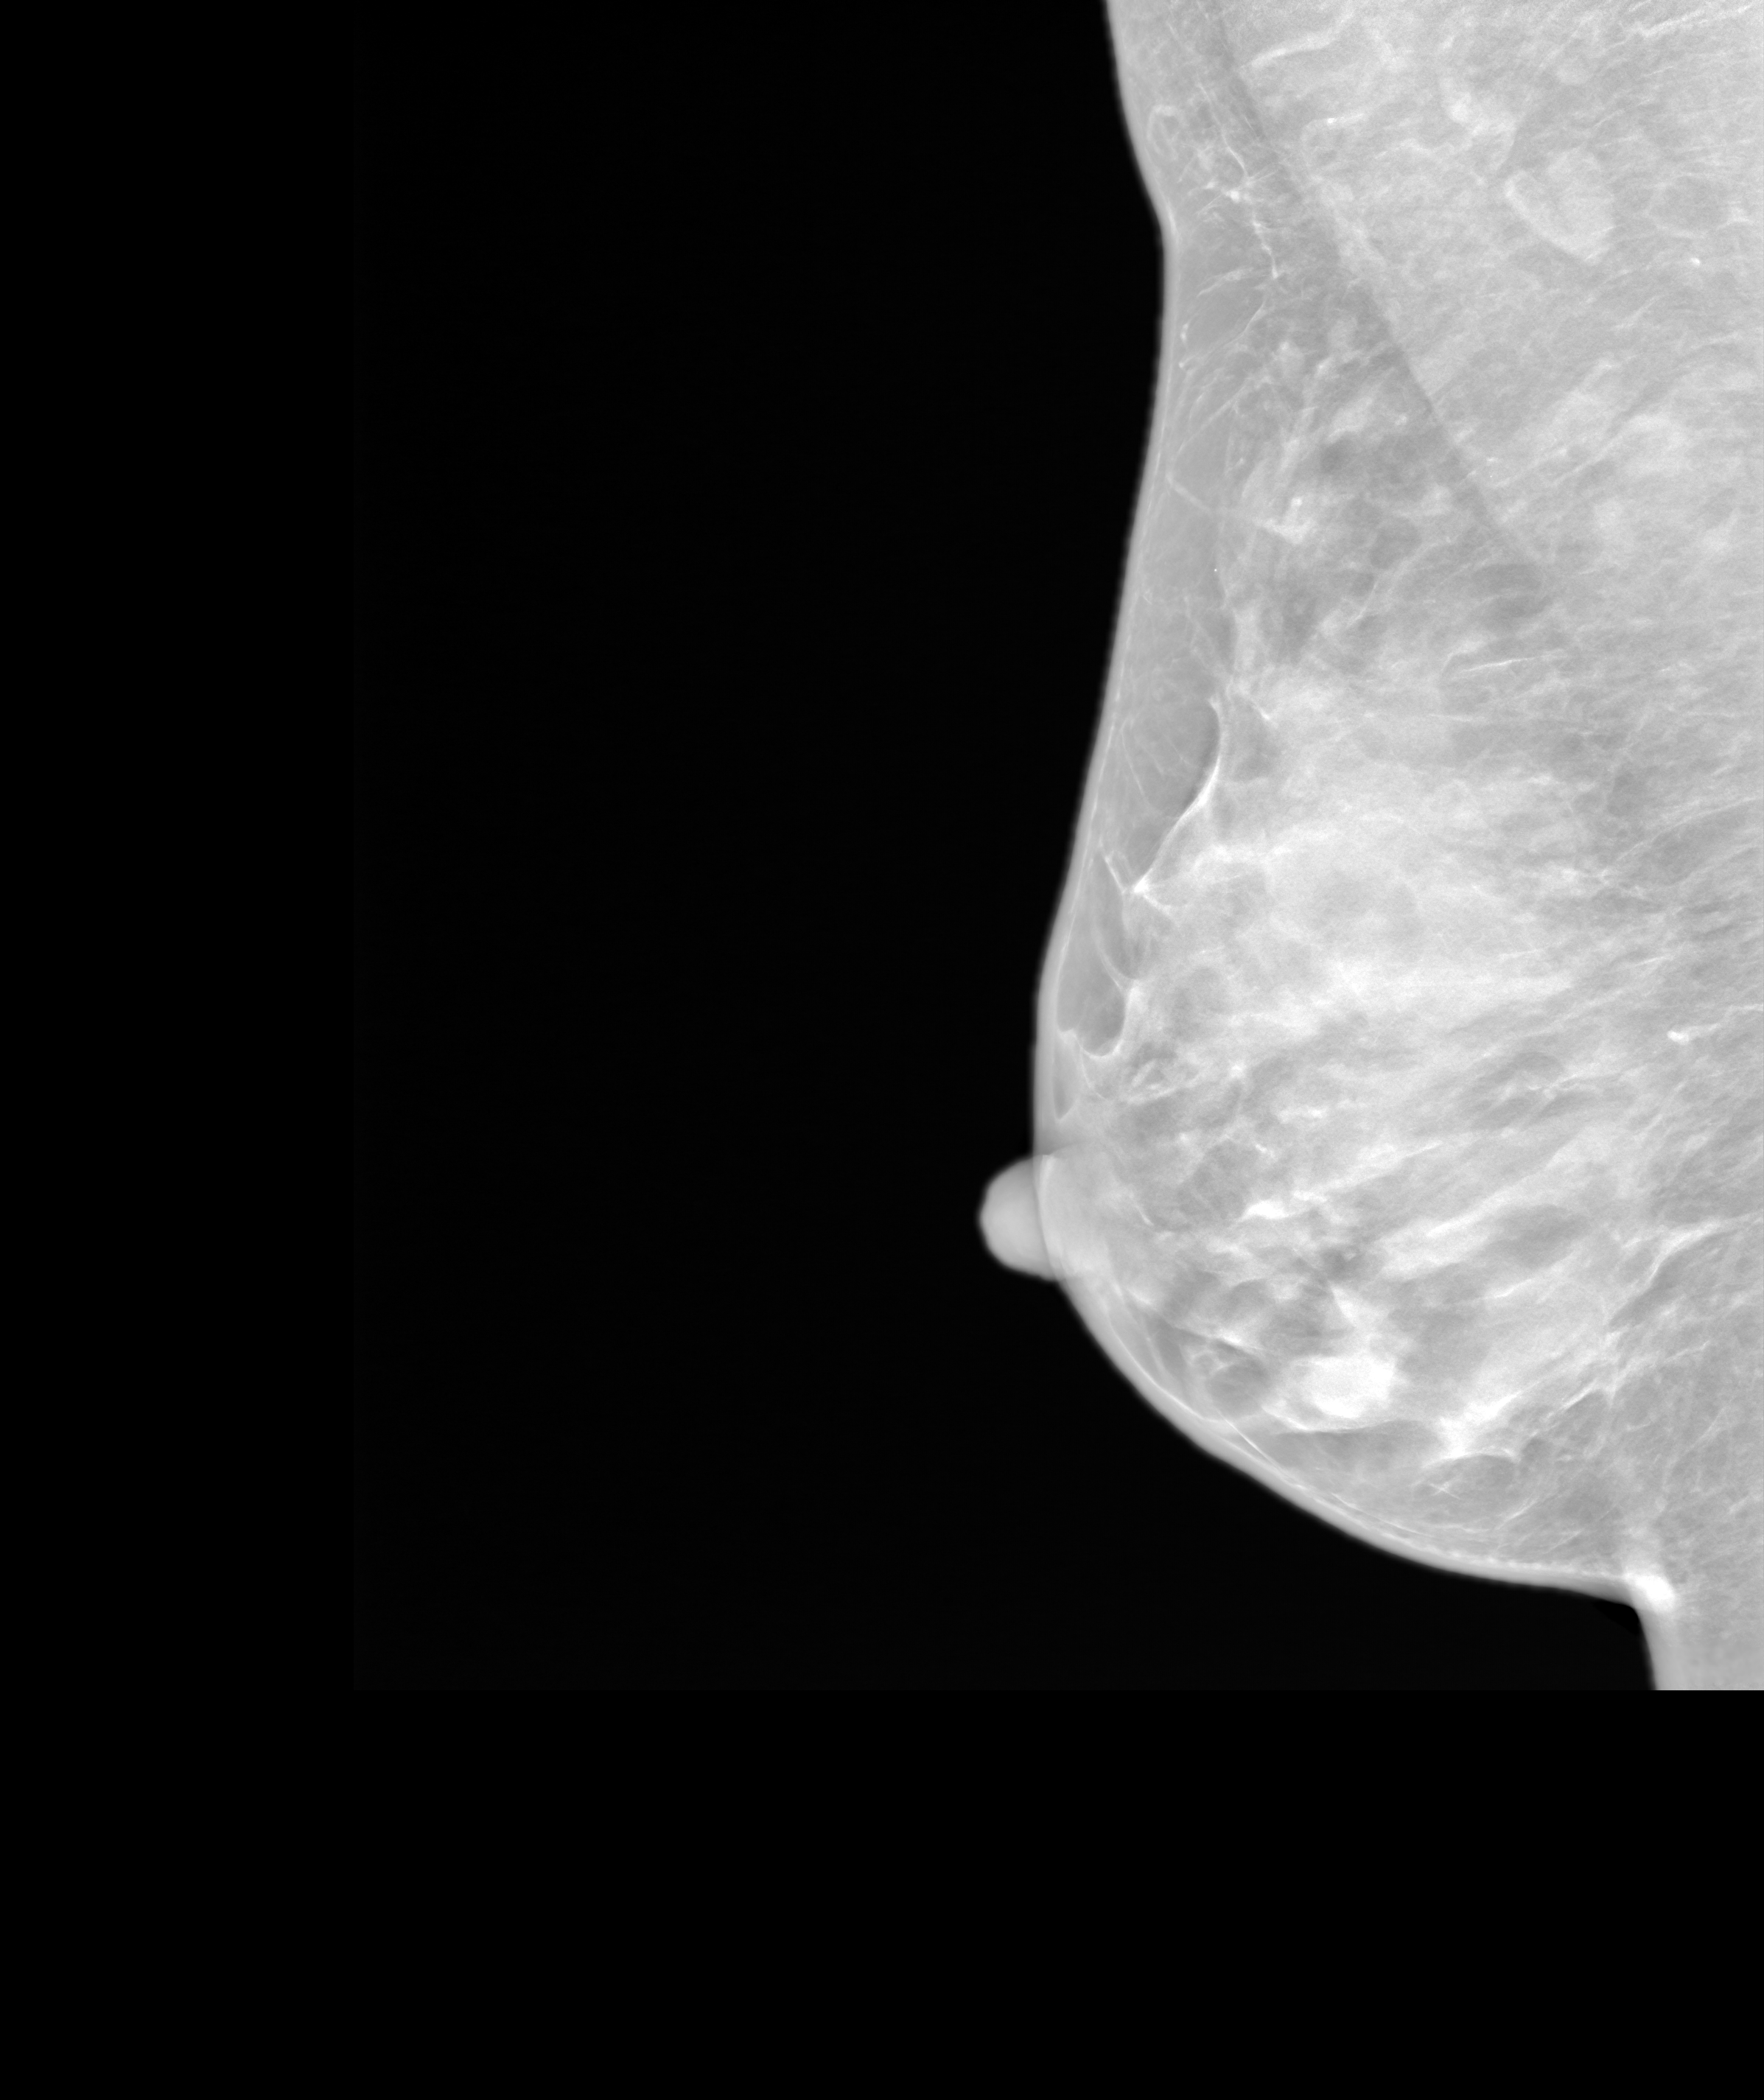
Annual screening mammography examination. Patient: female, 56 years.
Image type: synthesized 2-D view from tomosynthesis. Breast: right. Projection: medio-lateral oblique projection.